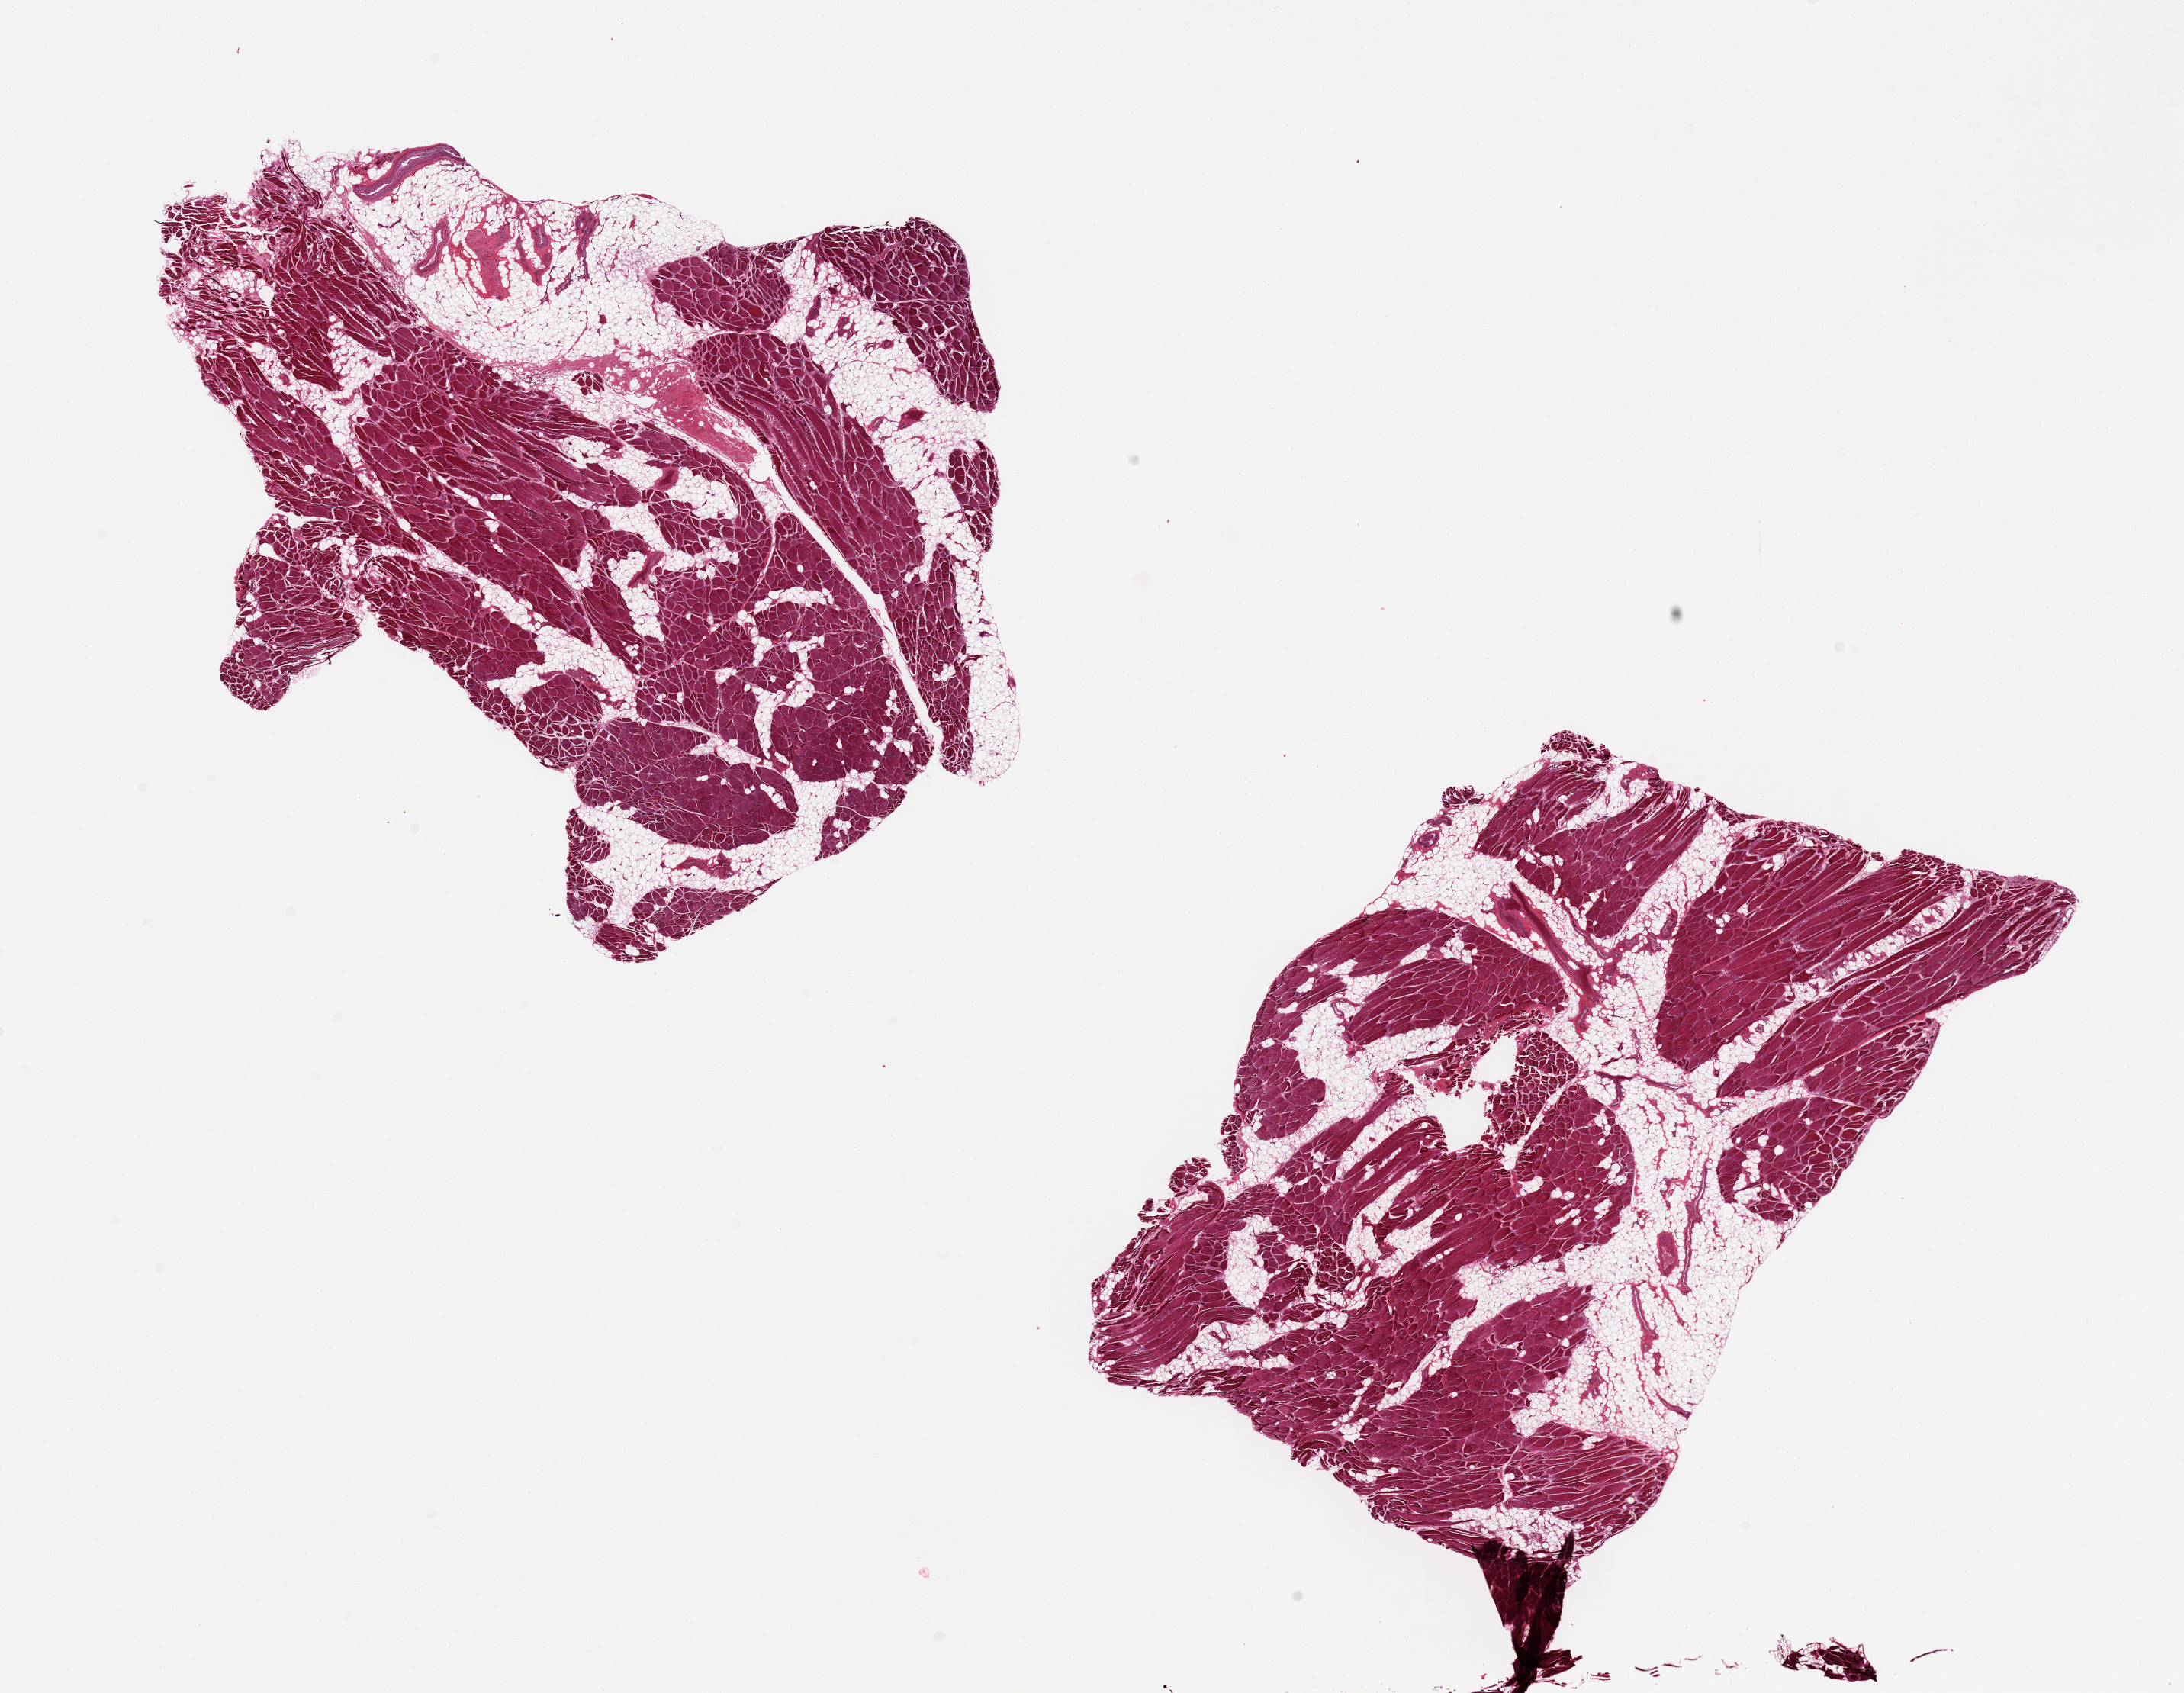
Haematoxylin and eosin whole-slide image, brightfield, shown as a low-resolution overview of the whole scanned area (about 22.6 x 17.5 mm). PAXgene-fixed paraffin-embedded (PFPE) section. Section of skeletal muscle (target tissue). Donor tissue sample.
* pathologist's review note for this sample: 2 pieces; each has 30% internal fat